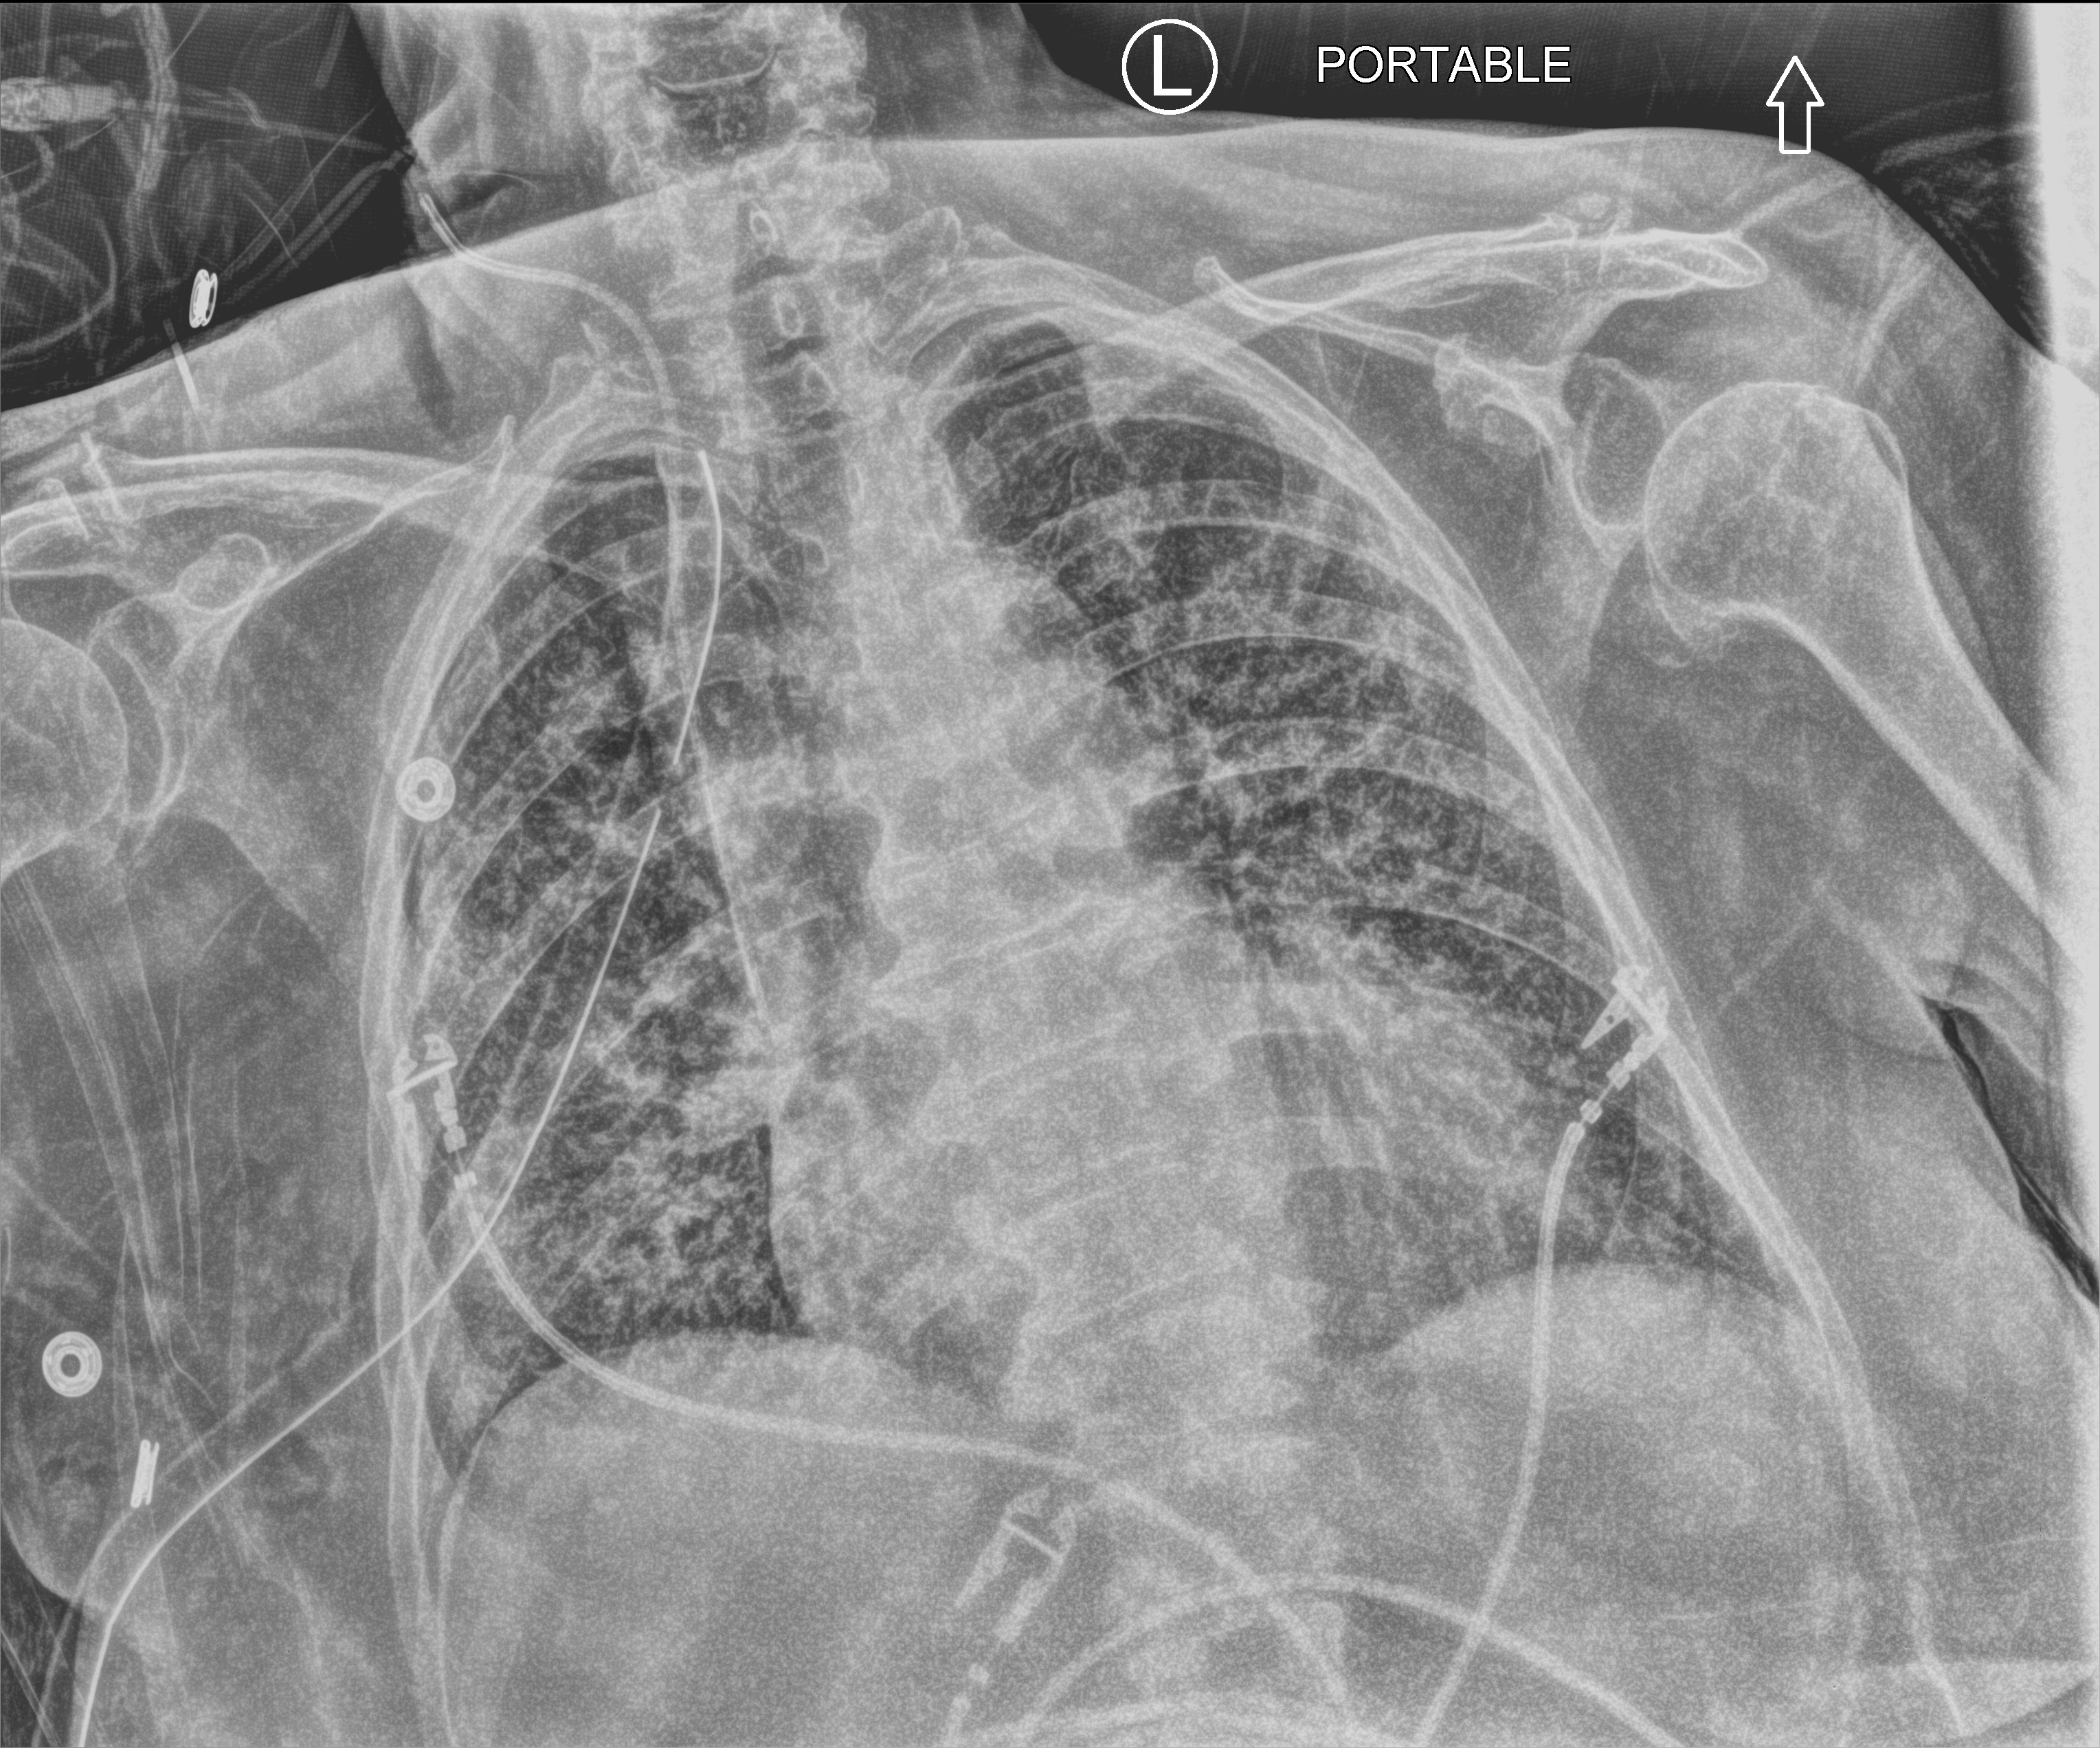
Portable chest radiograph. Patient hospitalised with COVID-19; female, aged 75–90 years.
Hospital-stay facts (about this admission, not read from this image; timing relative to this image not recorded): length of hospital stay: 56 days.